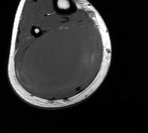
MRI of an extremity soft-tissue mass, one axial slice; position 55 of 76 along the scan axis; MR volume resampled by the dataset authors to the PET/CT grid (not the native acquisition matrix); 148 × 133 image matrix, field of view 145 × 130 mm. Male patient. From the clinical record (not read from this slice): histological type: liposarcoma - round cell; grade: high; site of the primary tumour: right calf.
Structures marked on this image (expert contour drawn on MRI and transferred to this co-registered scan by the dataset authors):
- gross tumour volume (mass): box from (x=15, y=21) to (x=101, y=95) px